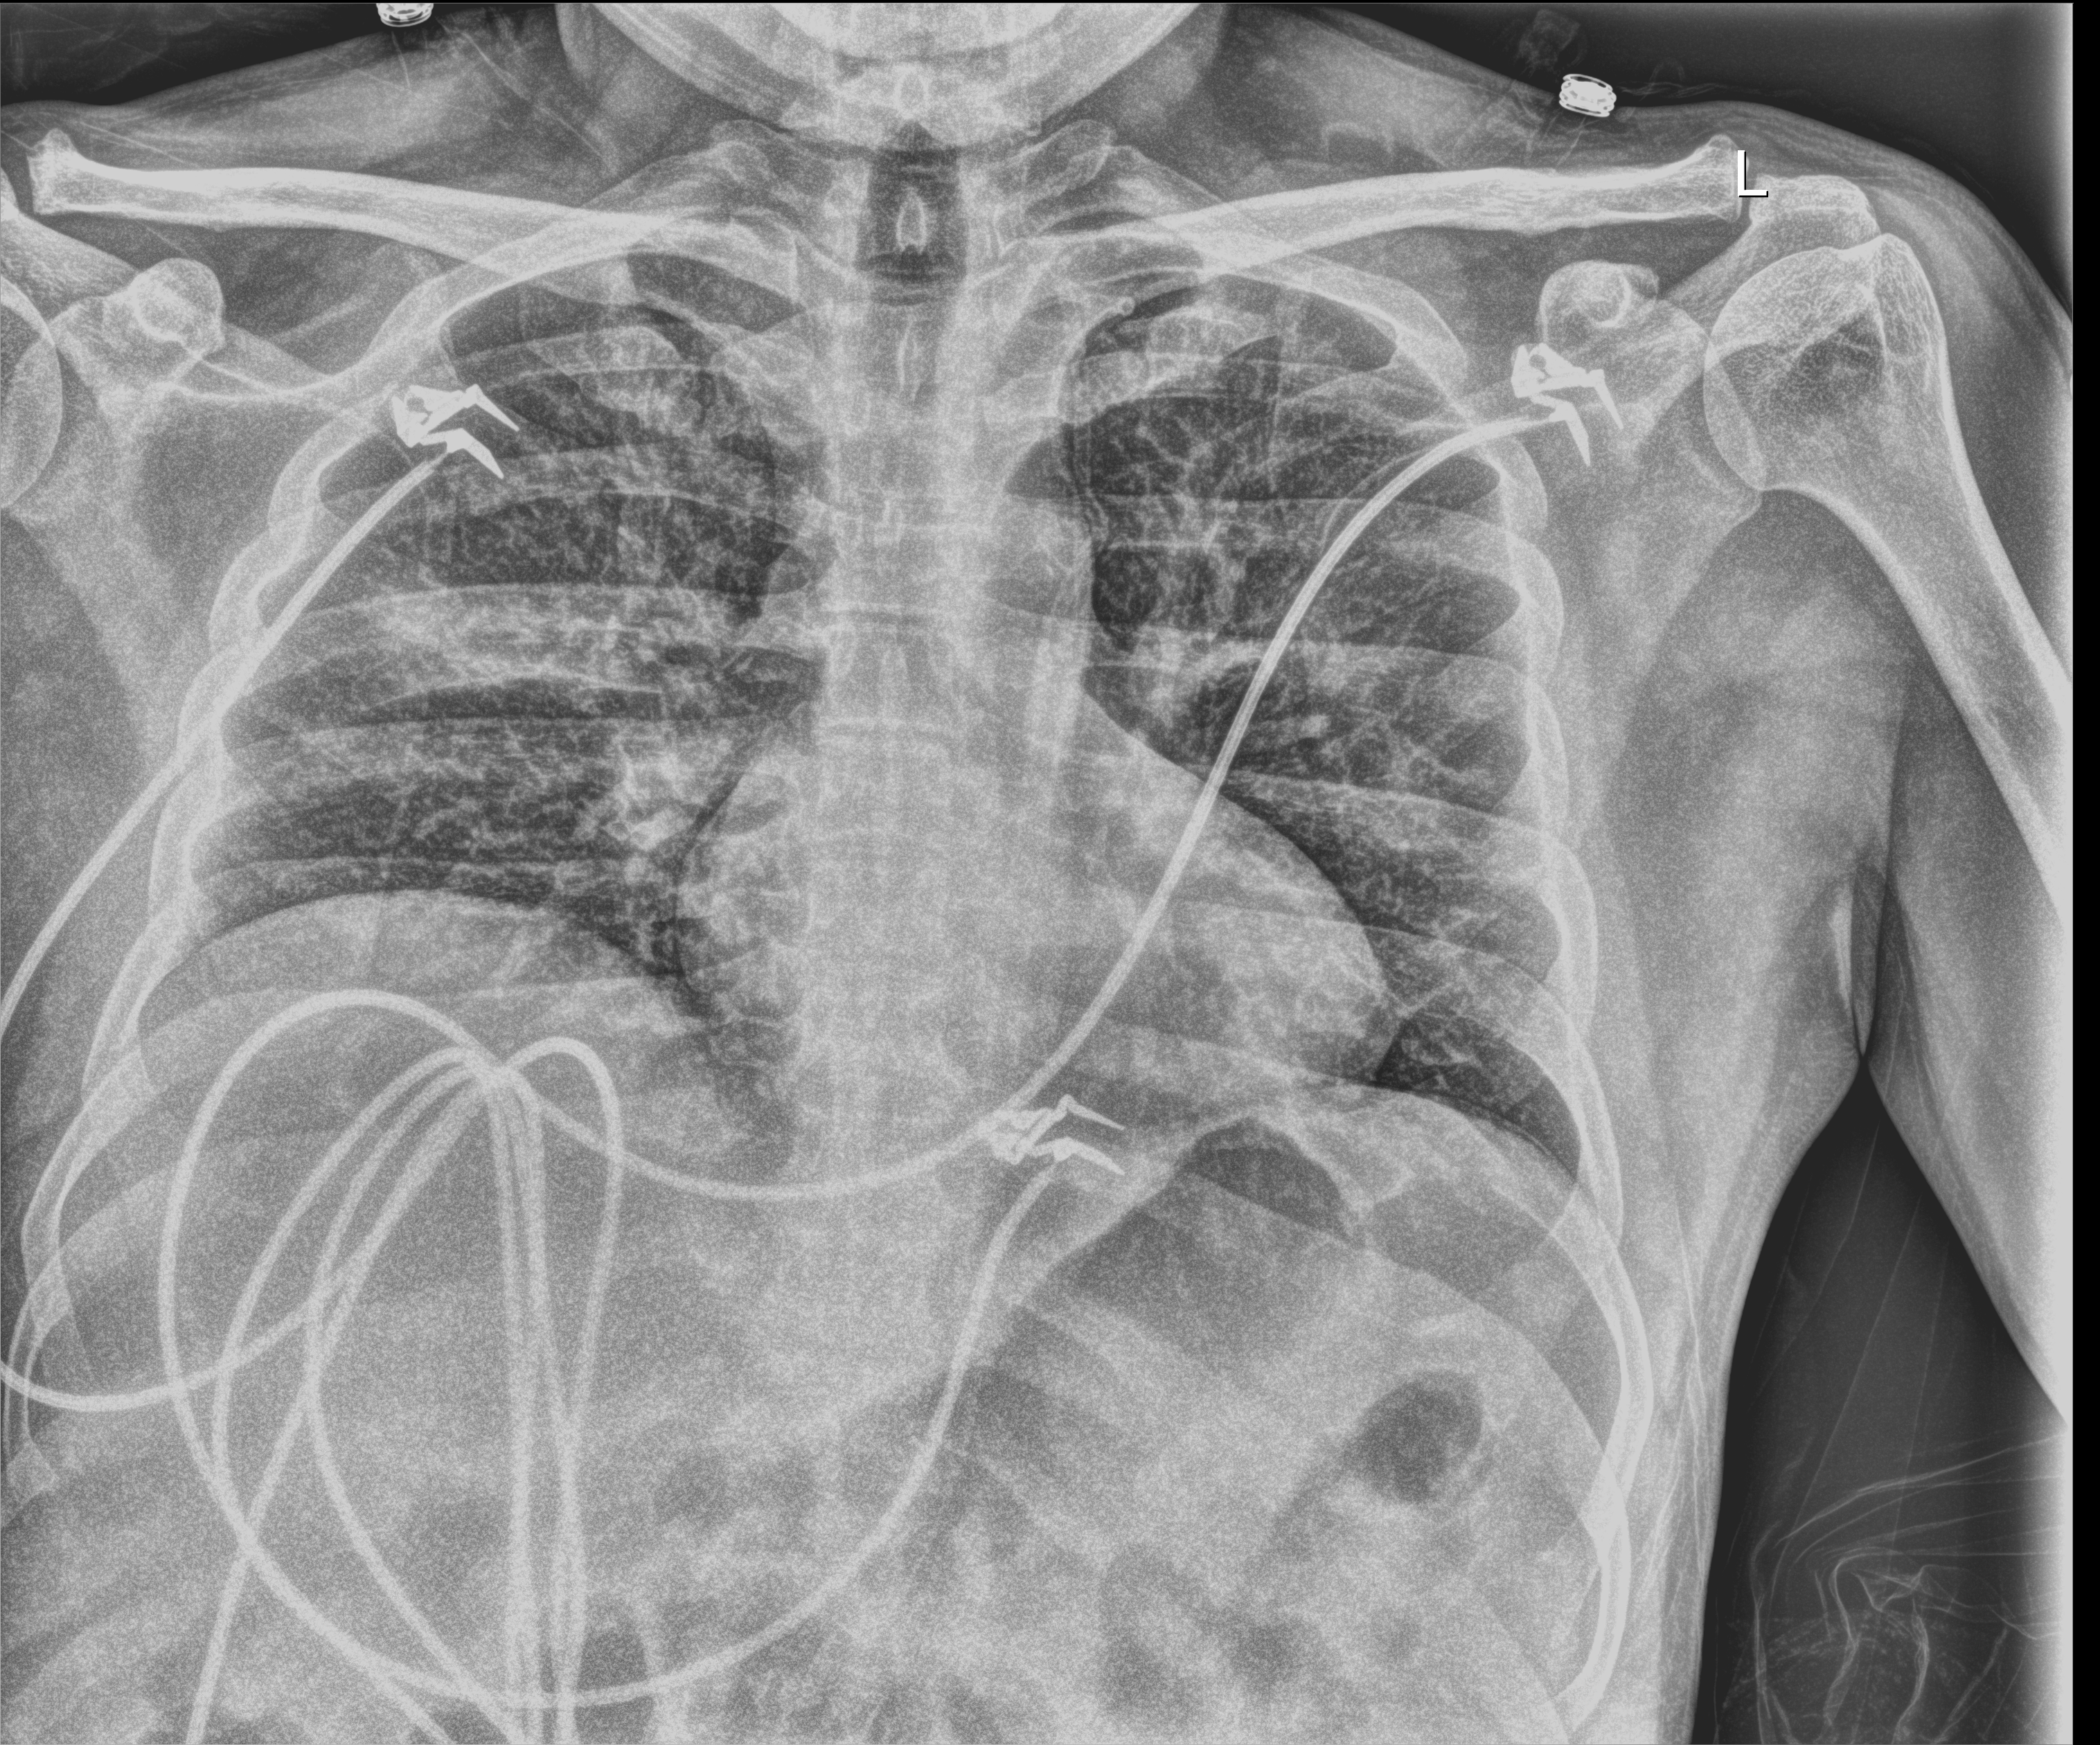
Chest radiograph; anteroposterior (AP) projection. Patient hospitalised with COVID-19, aged 18–59 years.
From the hospital-stay record, not from the radiograph (when in the stay this image was taken is not recorded):
- COPD (admission record): no
- admitted to intensive care during this hospital stay: no
- mechanically ventilated during this hospital stay: no